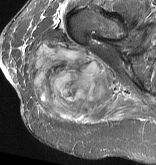
MRI of an extremity soft-tissue mass, one axial slice. Position 33 of 57 along the scan axis. STIR. MR volume resampled by the dataset authors to the PET/CT grid (not the native acquisition matrix). 3.27 mm slice thickness. 156 × 165 image matrix, field of view 152 × 161 mm. Female patient. From the clinical record (not read from this slice): histological type: epithelioid sarcoma with vascular differentiation; site of the primary tumour: right buttock.
Annotated regions visible in this slice (expert contour drawn on MRI and transferred to this co-registered scan by the dataset authors):
- gross tumour volume (mass): bounding box (x1, y1, x2, y2) in pixels: (26, 41, 112, 120)